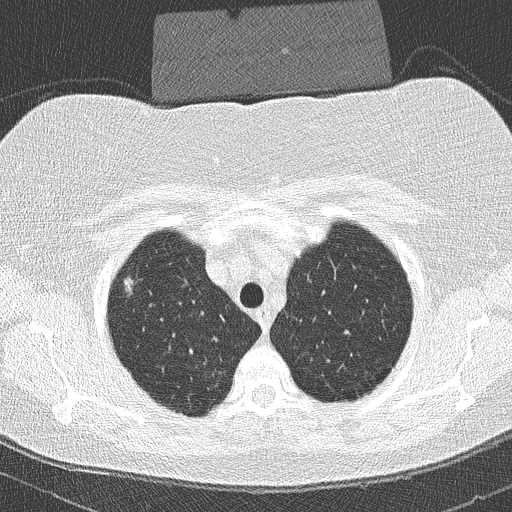
Chest CT (low-dose screening protocol), one axial image; second annual screen; lung window (W 1500 / L -600 HU); slice 38 of 293 in the series. Female, age 58 years at enrolment.
Expert-annotated lung lesion, box from (x=110, y=270) to (x=150, y=304) px. The screening reader recorded 2 non-calcified nodules or masses ≥4 mm on this exam (right upper lobe, right upper lobe); which of them this box marks is not recorded. Official screen result: positive, other.